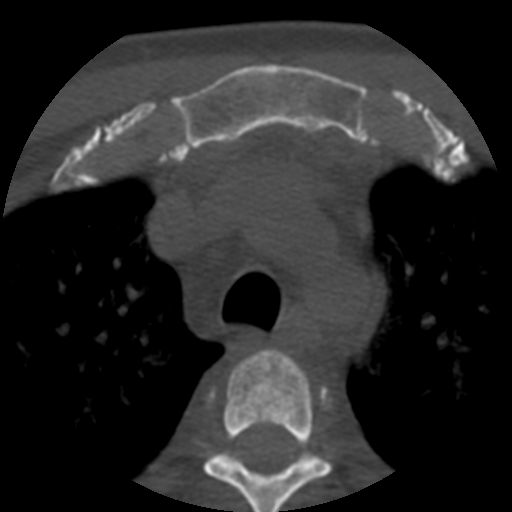
CT including the spine, one axial slice; position 412 of 508 along the scan axis; 120 kVp; bone window (W 1800 / L 400 HU); 1.25 mm slice thickness; 512 × 512 image matrix, field of view 160 × 160 mm. Patient age 57 years. Case-level facts recorded for this patient, not image findings: primary cancer: prostate.
Structures marked on this image (semi-automatic segmentation, software-assisted and operator-edited):
- T3 vertebra: bounding box [x1, y1, x2, y2] px = [203, 348, 333, 512]
- T4 vertebra: [234, 456, 317, 464]